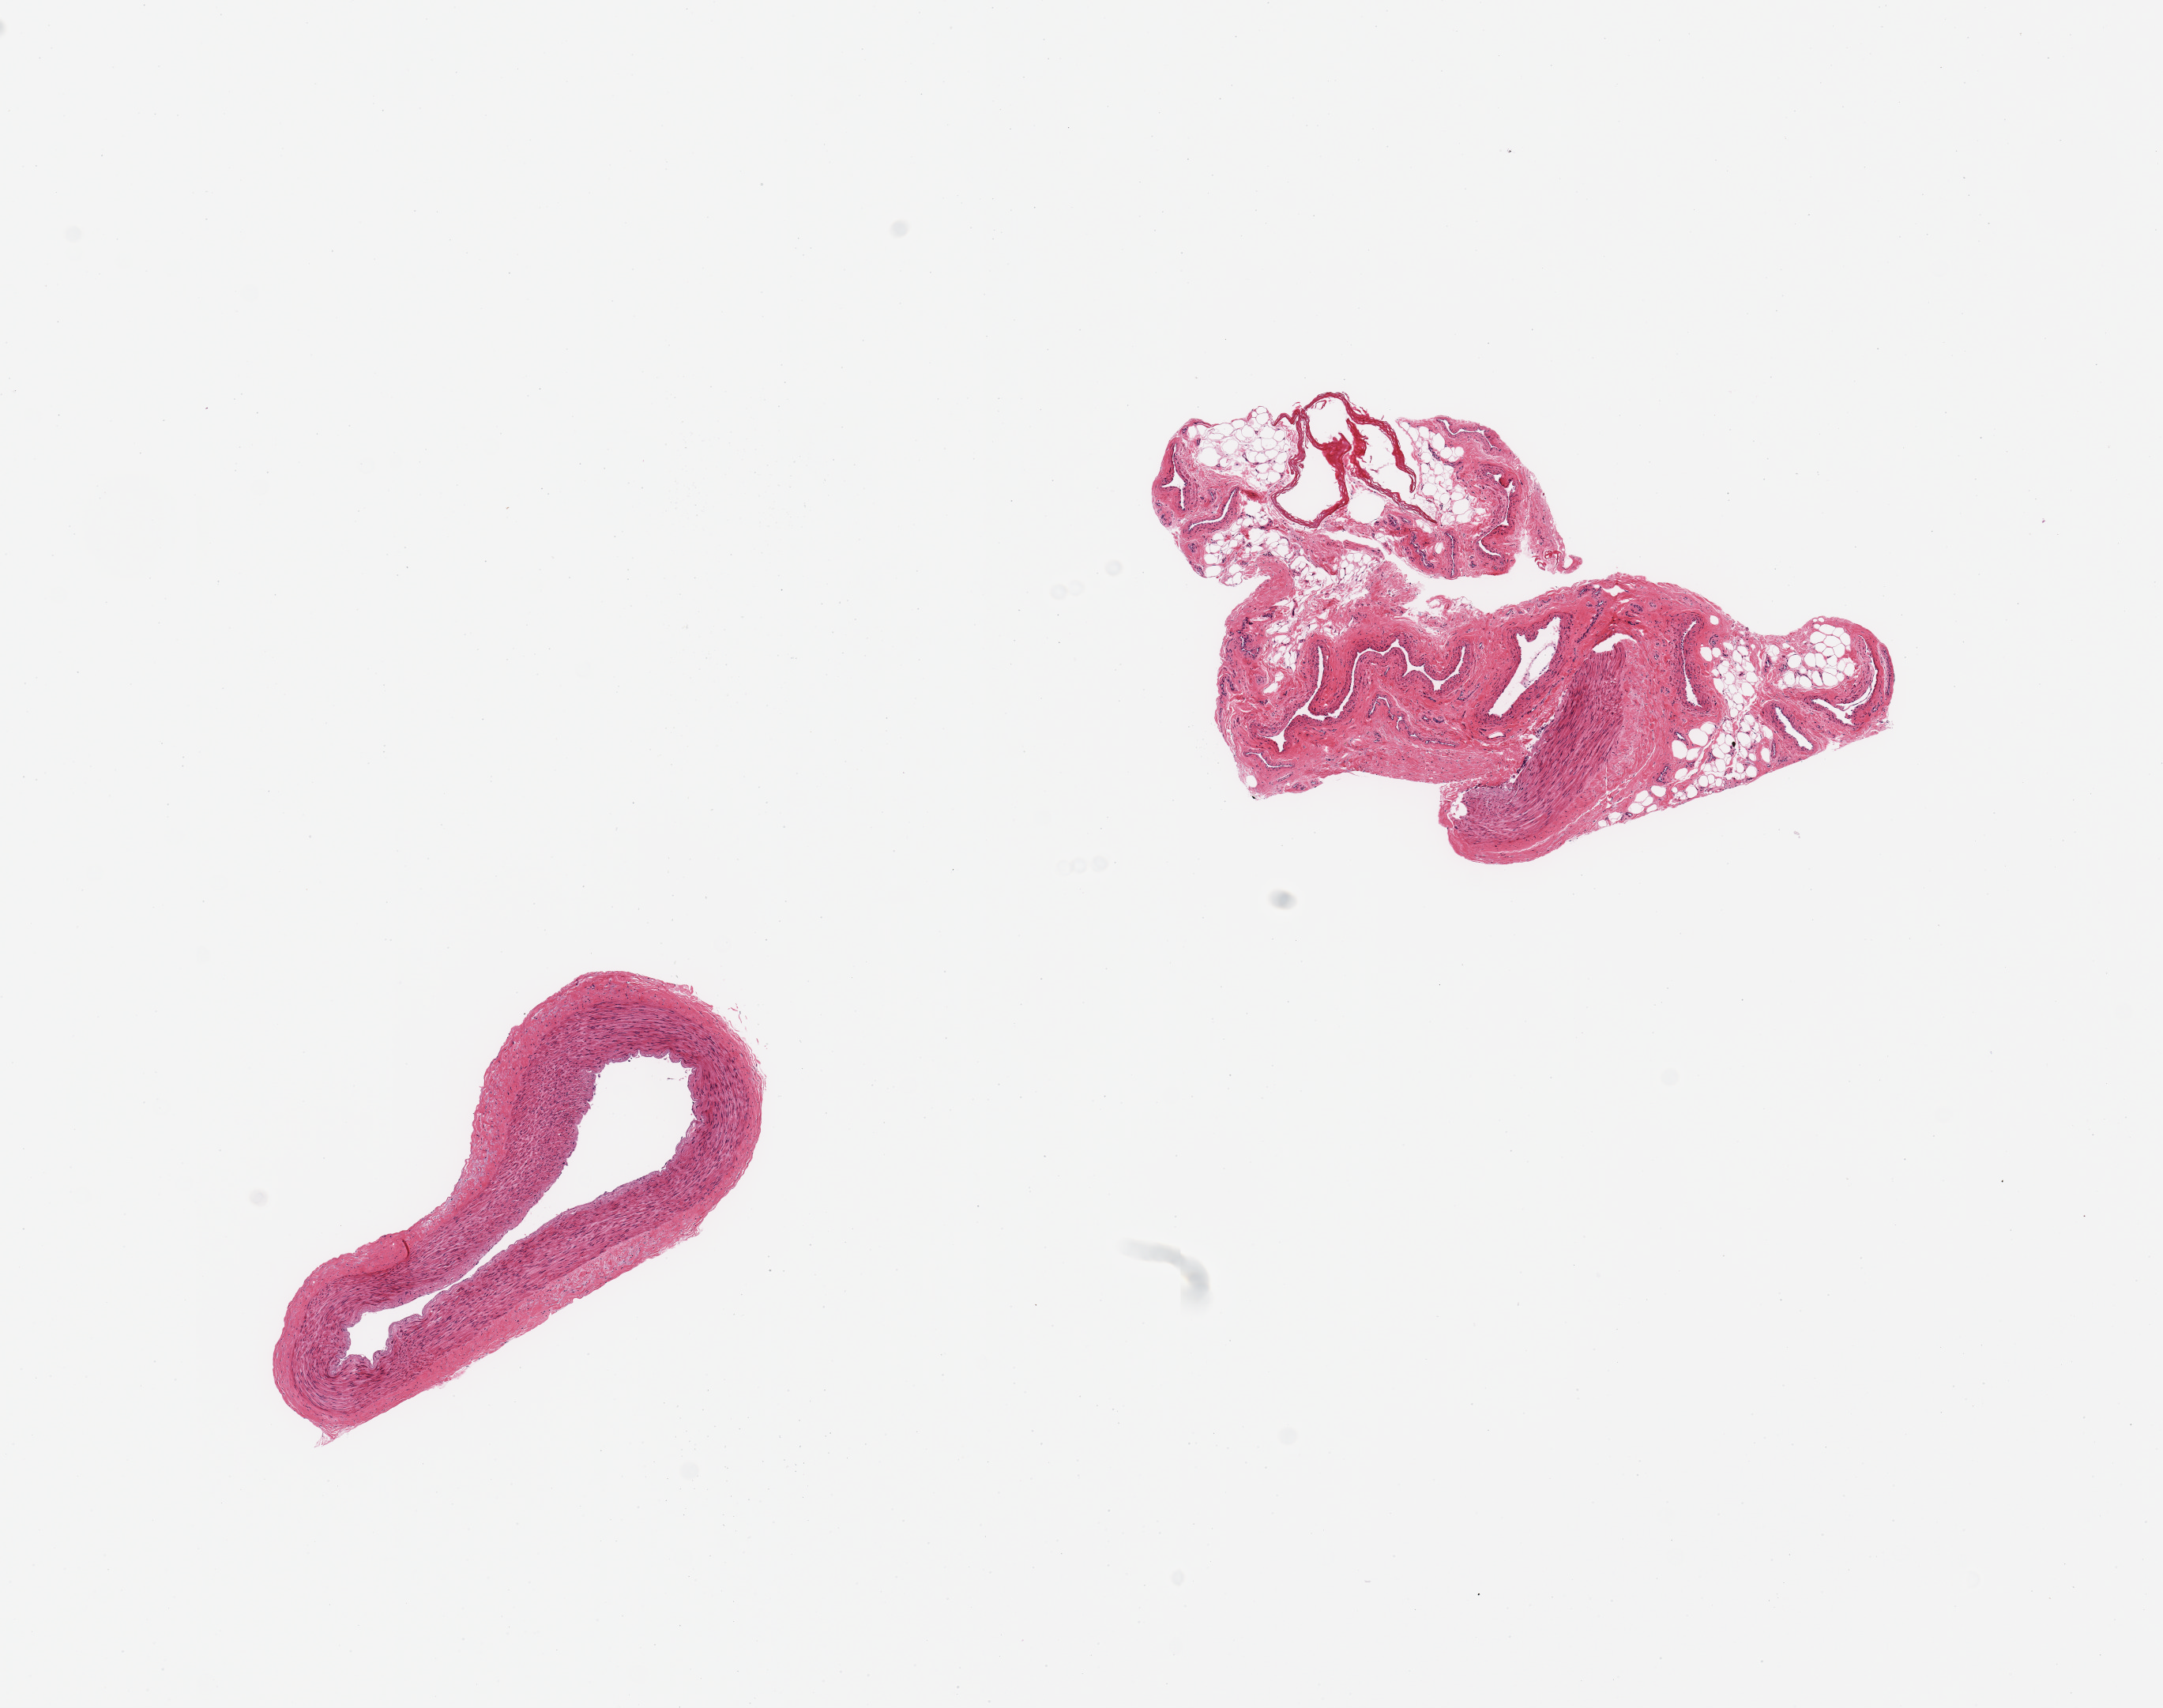
Digitized haematoxylin and eosin-stained section — low-resolution overview of the scanned area, about 10.8 x 8.6 mm, PAXgene-fixed, paraffin-embedded tissue, section of tibial artery (target tissue), donor tissue sample. Donor: male.
• pathologist's review note for this sample: 2 pieces; one is pristine vessel, the other is primarily peripheral nerve/adipose/connective tissue; Sample with caution